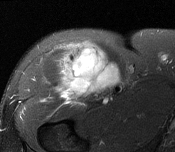
MRI of an extremity soft-tissue mass, one axial slice; slice 107 of 116 in the series (ordered by position); T2-weighted fat-saturated; MR volume resampled by the dataset authors to the PET/CT grid (not the native acquisition matrix); 3.27 mm slice thickness; 175 × 152 image matrix. Male patient. From the clinical record (not read from this slice): histological type: pleiomorphic leiomyosarcoma; grade: intermediate; site of the primary tumour: right thigh.
Structures marked on this image (expert contour drawn on MRI and transferred to this co-registered scan by the dataset authors):
- gross tumour volume including surrounding oedema: box from (x=58, y=43) to (x=119, y=98) px
- gross tumour volume (mass): (x=63, y=52)–(x=118, y=96)